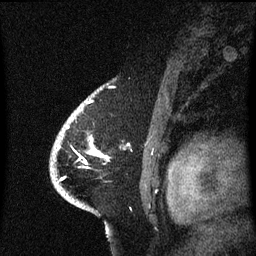
Breast MRI (dynamic contrast-enhanced), one sagittal slice. Slice 48 of 60 in the series (ordered by position). Dynamic contrast-enhanced series, image 2 of 3 at this slice position (ordered by acquisition). 1.5 T. TE 4.2 ms, TR 8.4 ms. 256 × 256 image matrix, field of view 200 × 200 mm. Female patient, age 53 years. From the clinical record (not read from this slice): setting: breast cancer imaged before/during neoadjuvant chemotherapy; receptor status: HR-positive, HER2-negative.
Structures marked on this image (semi-automatically segmented with operator editing):
- analysis volume of interest (the breast-tissue region the enhancement analysis was run in; not a lesion): box from (x=51, y=108) to (x=109, y=201) px
- tumour enhancement mask (voxels above the 70 % enhancement threshold inside the analysis volume of interest): (x=90, y=150)–(x=103, y=157)